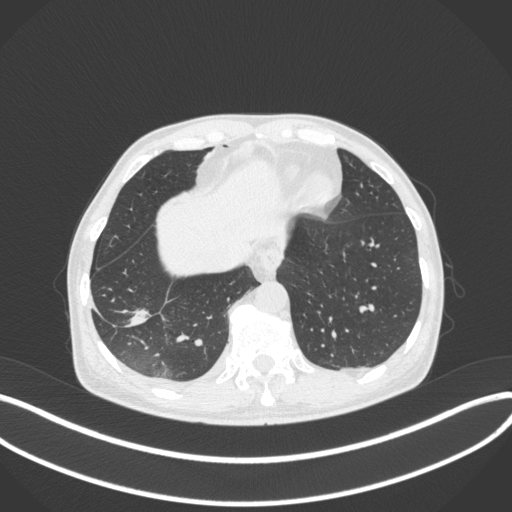
Chest CT, one axial slice; slice 83 of 385 in the series (ordered by position); lung window (W 1500 / L -600 HU); 512 × 512 image matrix, field of view 400 × 400 mm. Male patient, age 64 years. From the clinical record (not read from this slice): clinical TNM (as recorded): T3 N0 M0.
Annotated regions visible in this slice (bounding box drawn by a radiologist):
- lung tumour (recorded histology: adenocarcinoma): bounding box [x1, y1, x2, y2] px = [124, 302, 155, 332]